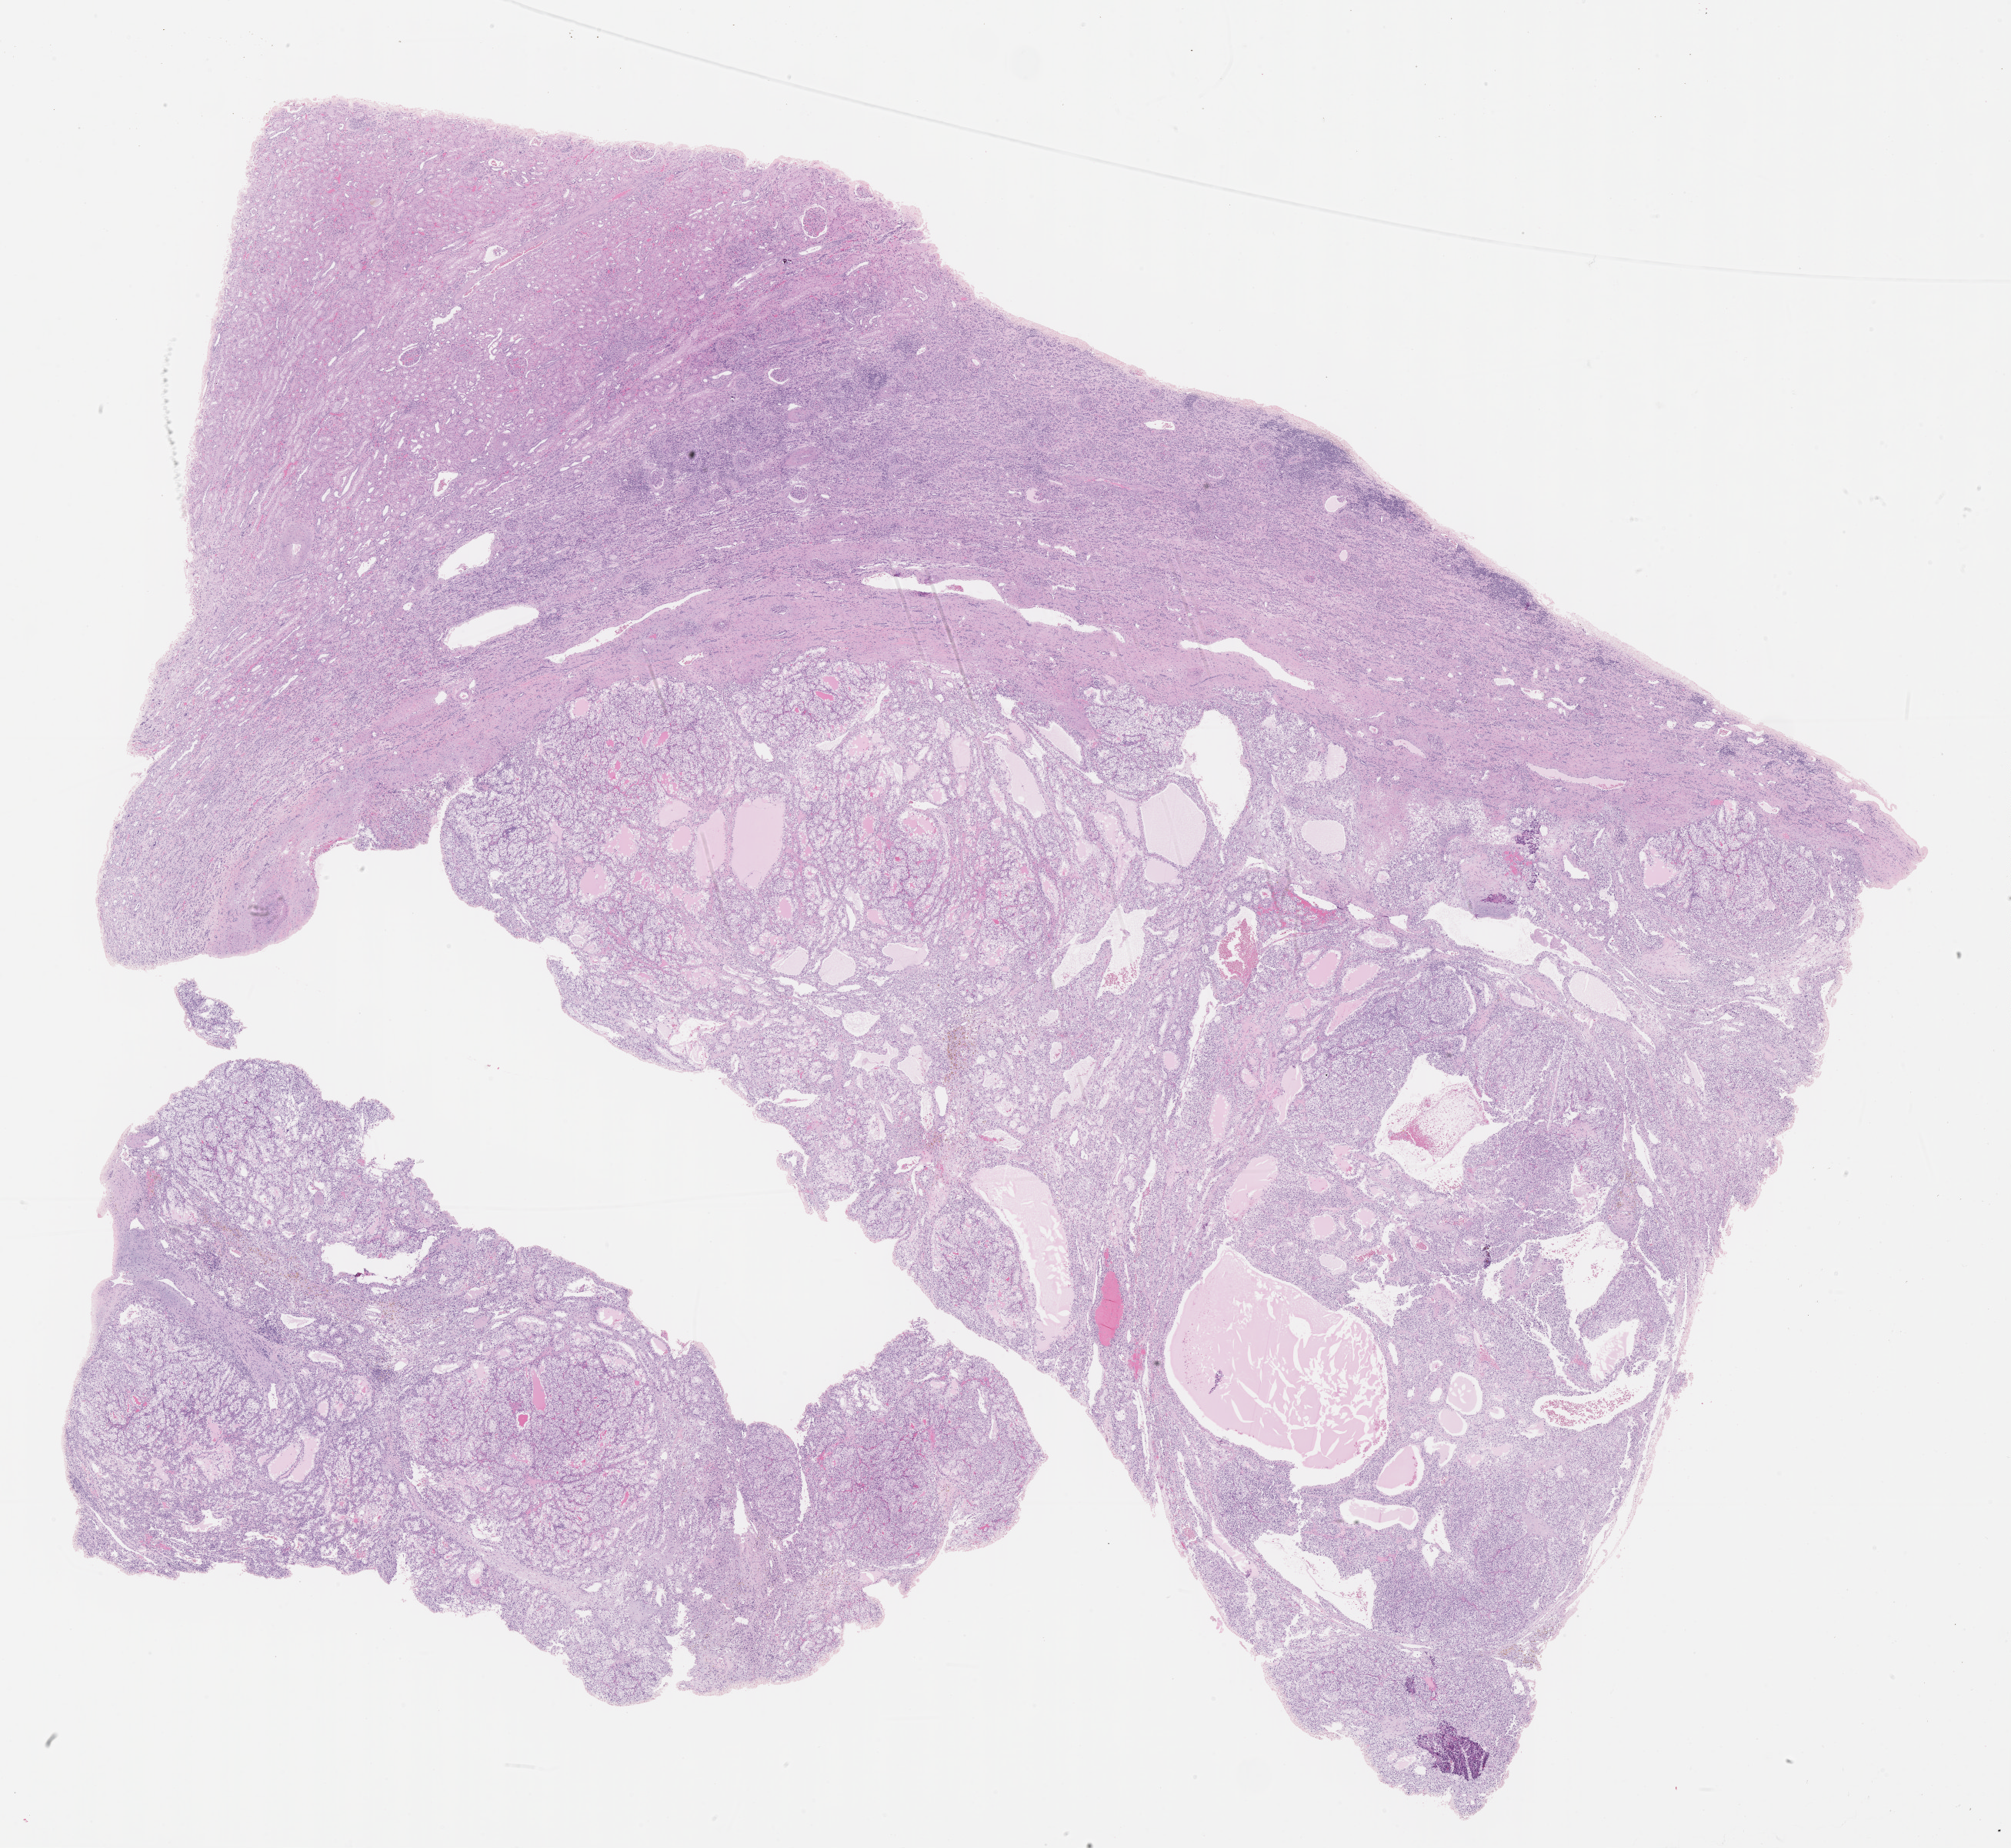
Digitized H&E tissue section (whole slide), shown as a low-resolution overview of the whole scanned area (about 21.1 x 19.4 mm); FFPE section; kidney, primary tumour sample. Patient: male, age at initial diagnosis 50 years. Histologic grade: G3 (poorly differentiated).
- pathologic diagnosis: Clear cell adenocarcinoma, NOS
- TNM: T1b NX M0
- AJCC pathologic stage: I